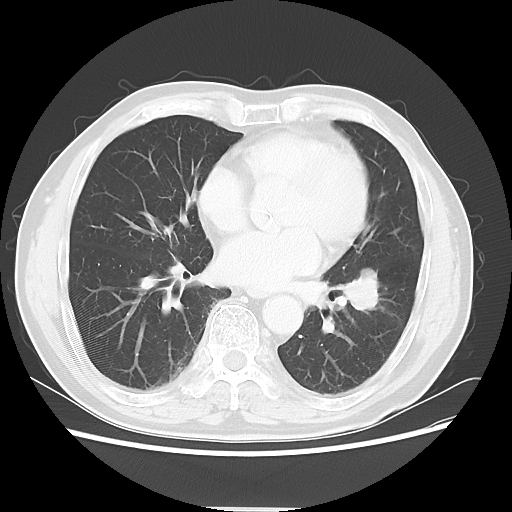
Chest CT, one axial slice; slice 25 of 64 in the series (ordered by position); 120 kVp; lung window (W 1500 / L -600 HU); 5 mm slice thickness; 512 × 512 image matrix, field of view 366 × 366 mm. Male patient, age 71 years. Case-level facts recorded for this patient, not image findings: clinical TNM (as recorded): T1c N1 M0; histopathological grade: G2-3.
Annotated regions visible in this slice (bounding box drawn by a radiologist):
- lung tumour (recorded histology: adenocarcinoma): bounding box (x1, y1, x2, y2) in pixels: (342, 264, 389, 321)